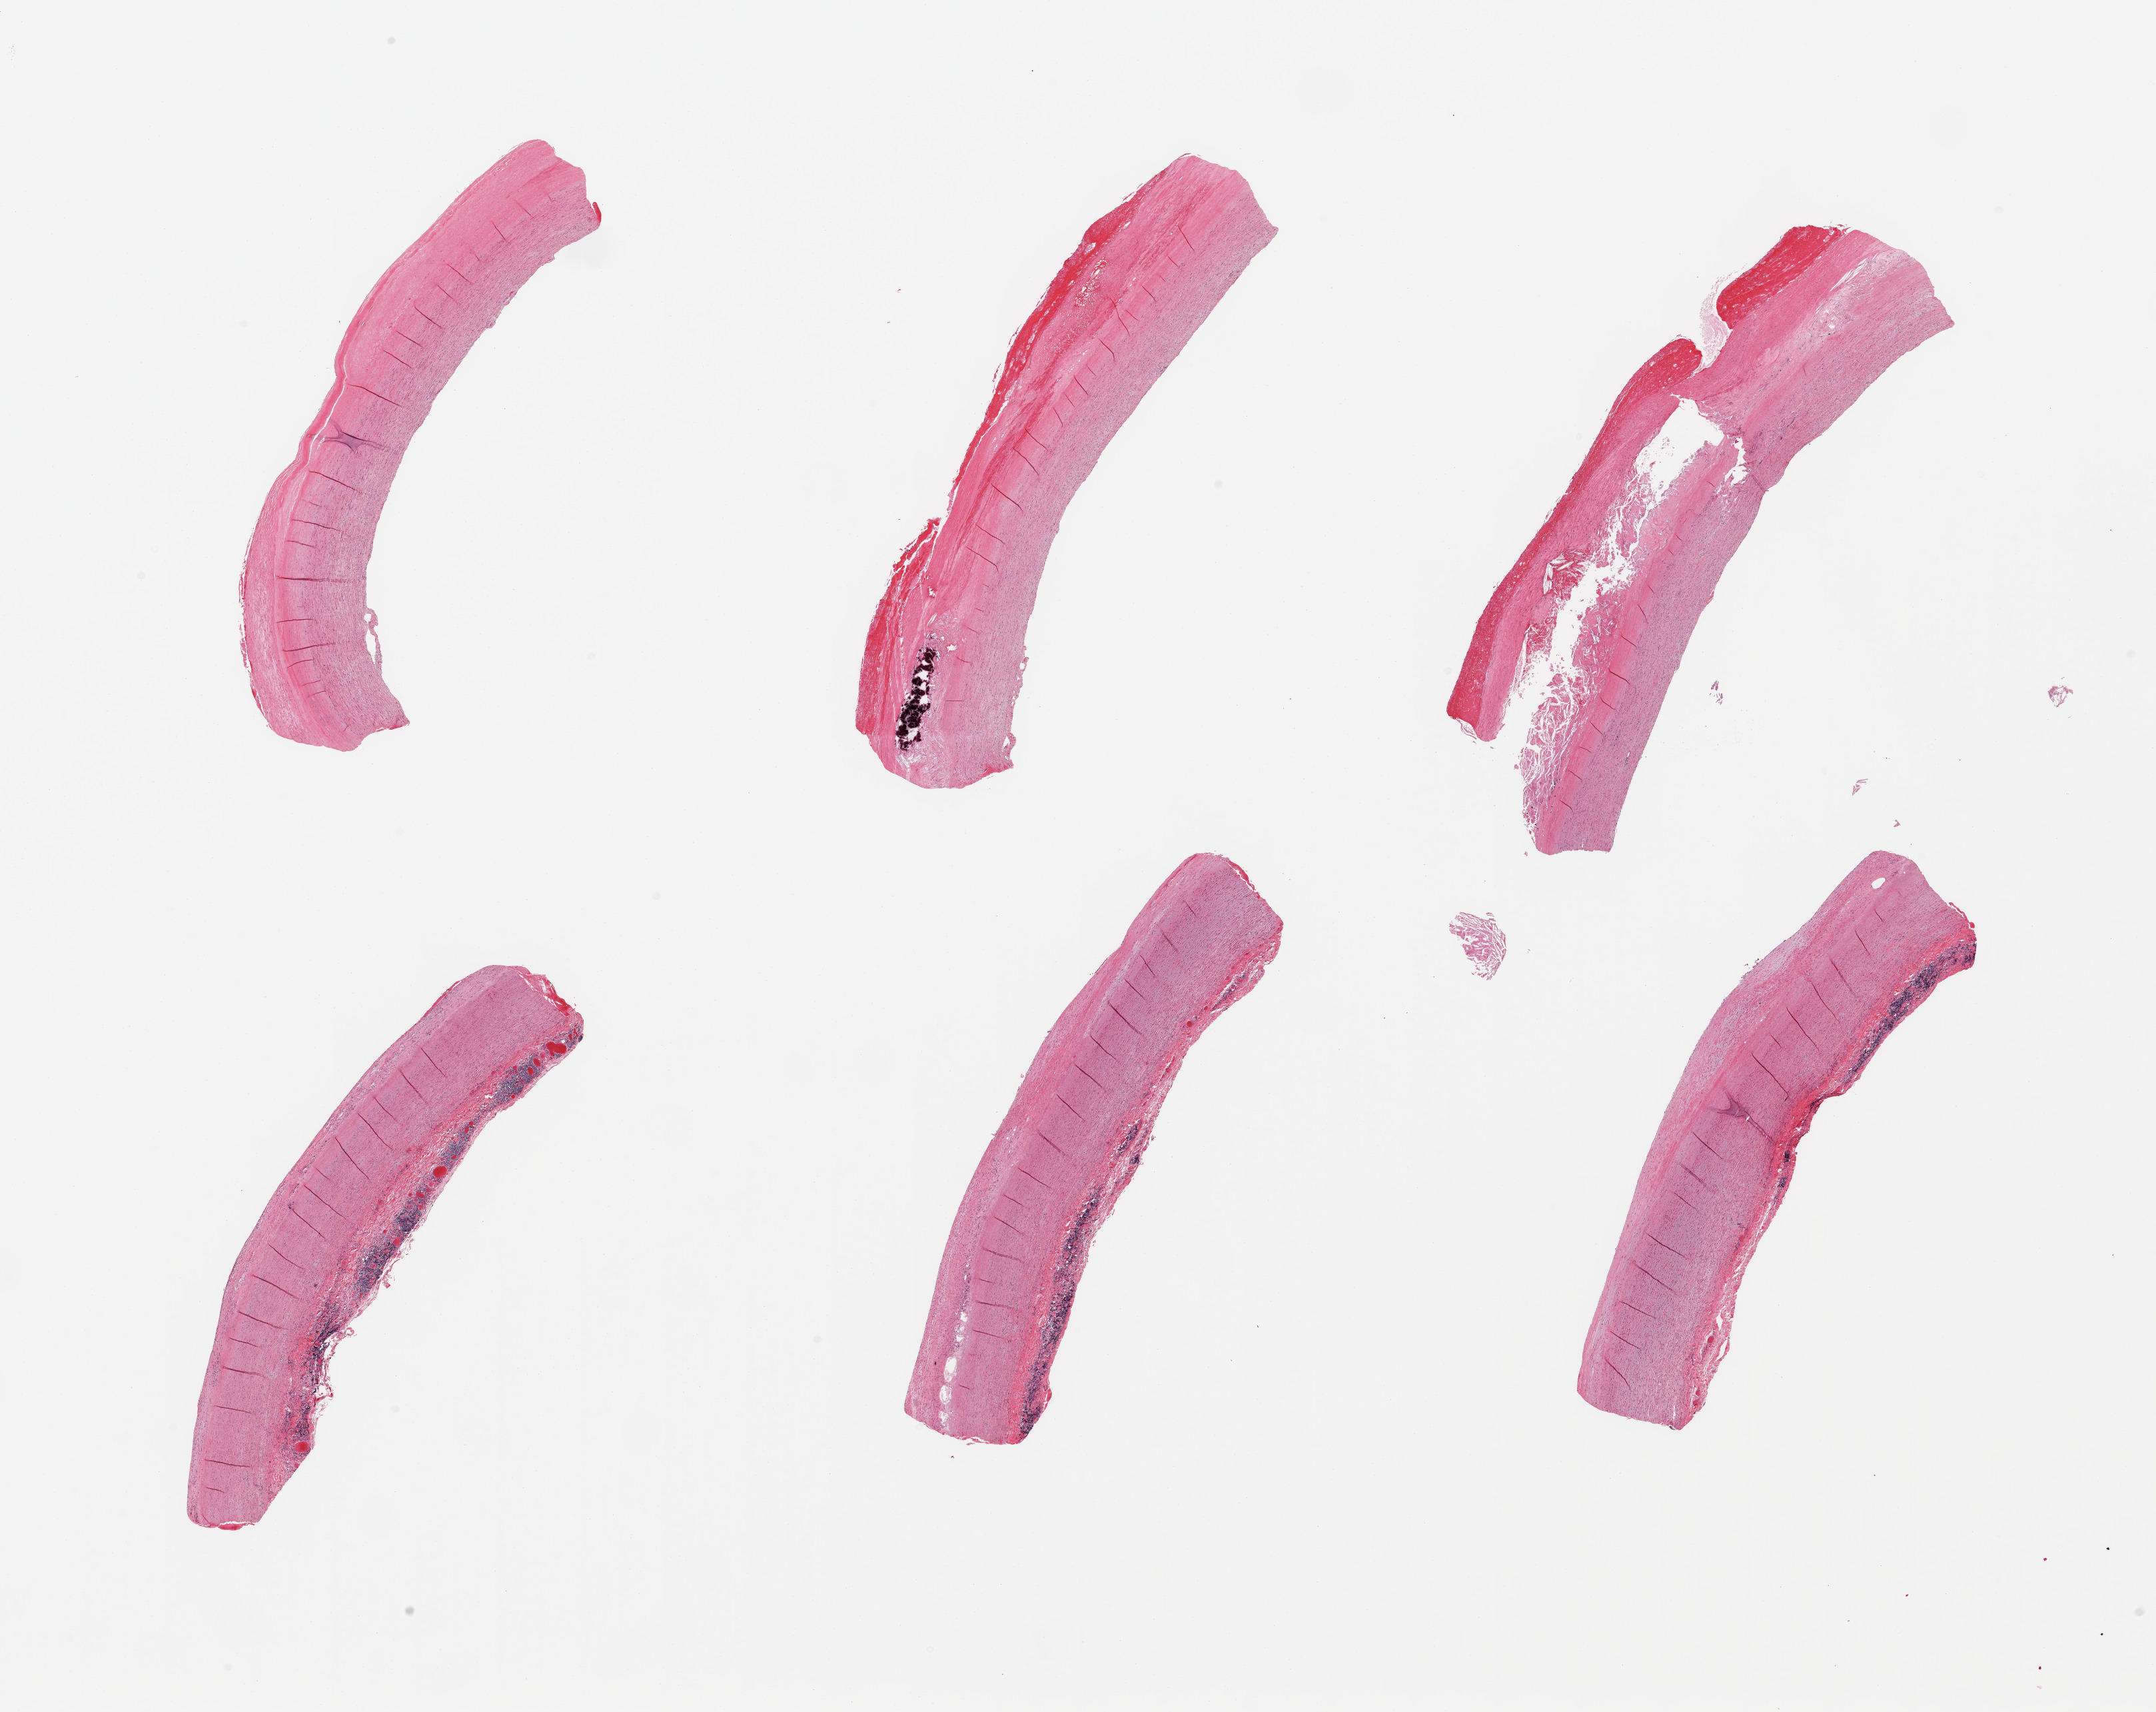
H&E whole-slide image, low-resolution overview of the scanned area, about 25.6 x 20.3 mm (acquisition: 20x scan), PAXgene-fixed, paraffin-embedded tissue, sampled site (target tissue): aorta, tissue donor sample. Female donor.
Reviewer comment on this tissue sample: 6 pieces focally calcified atherosis up to ~1-1.5mm.